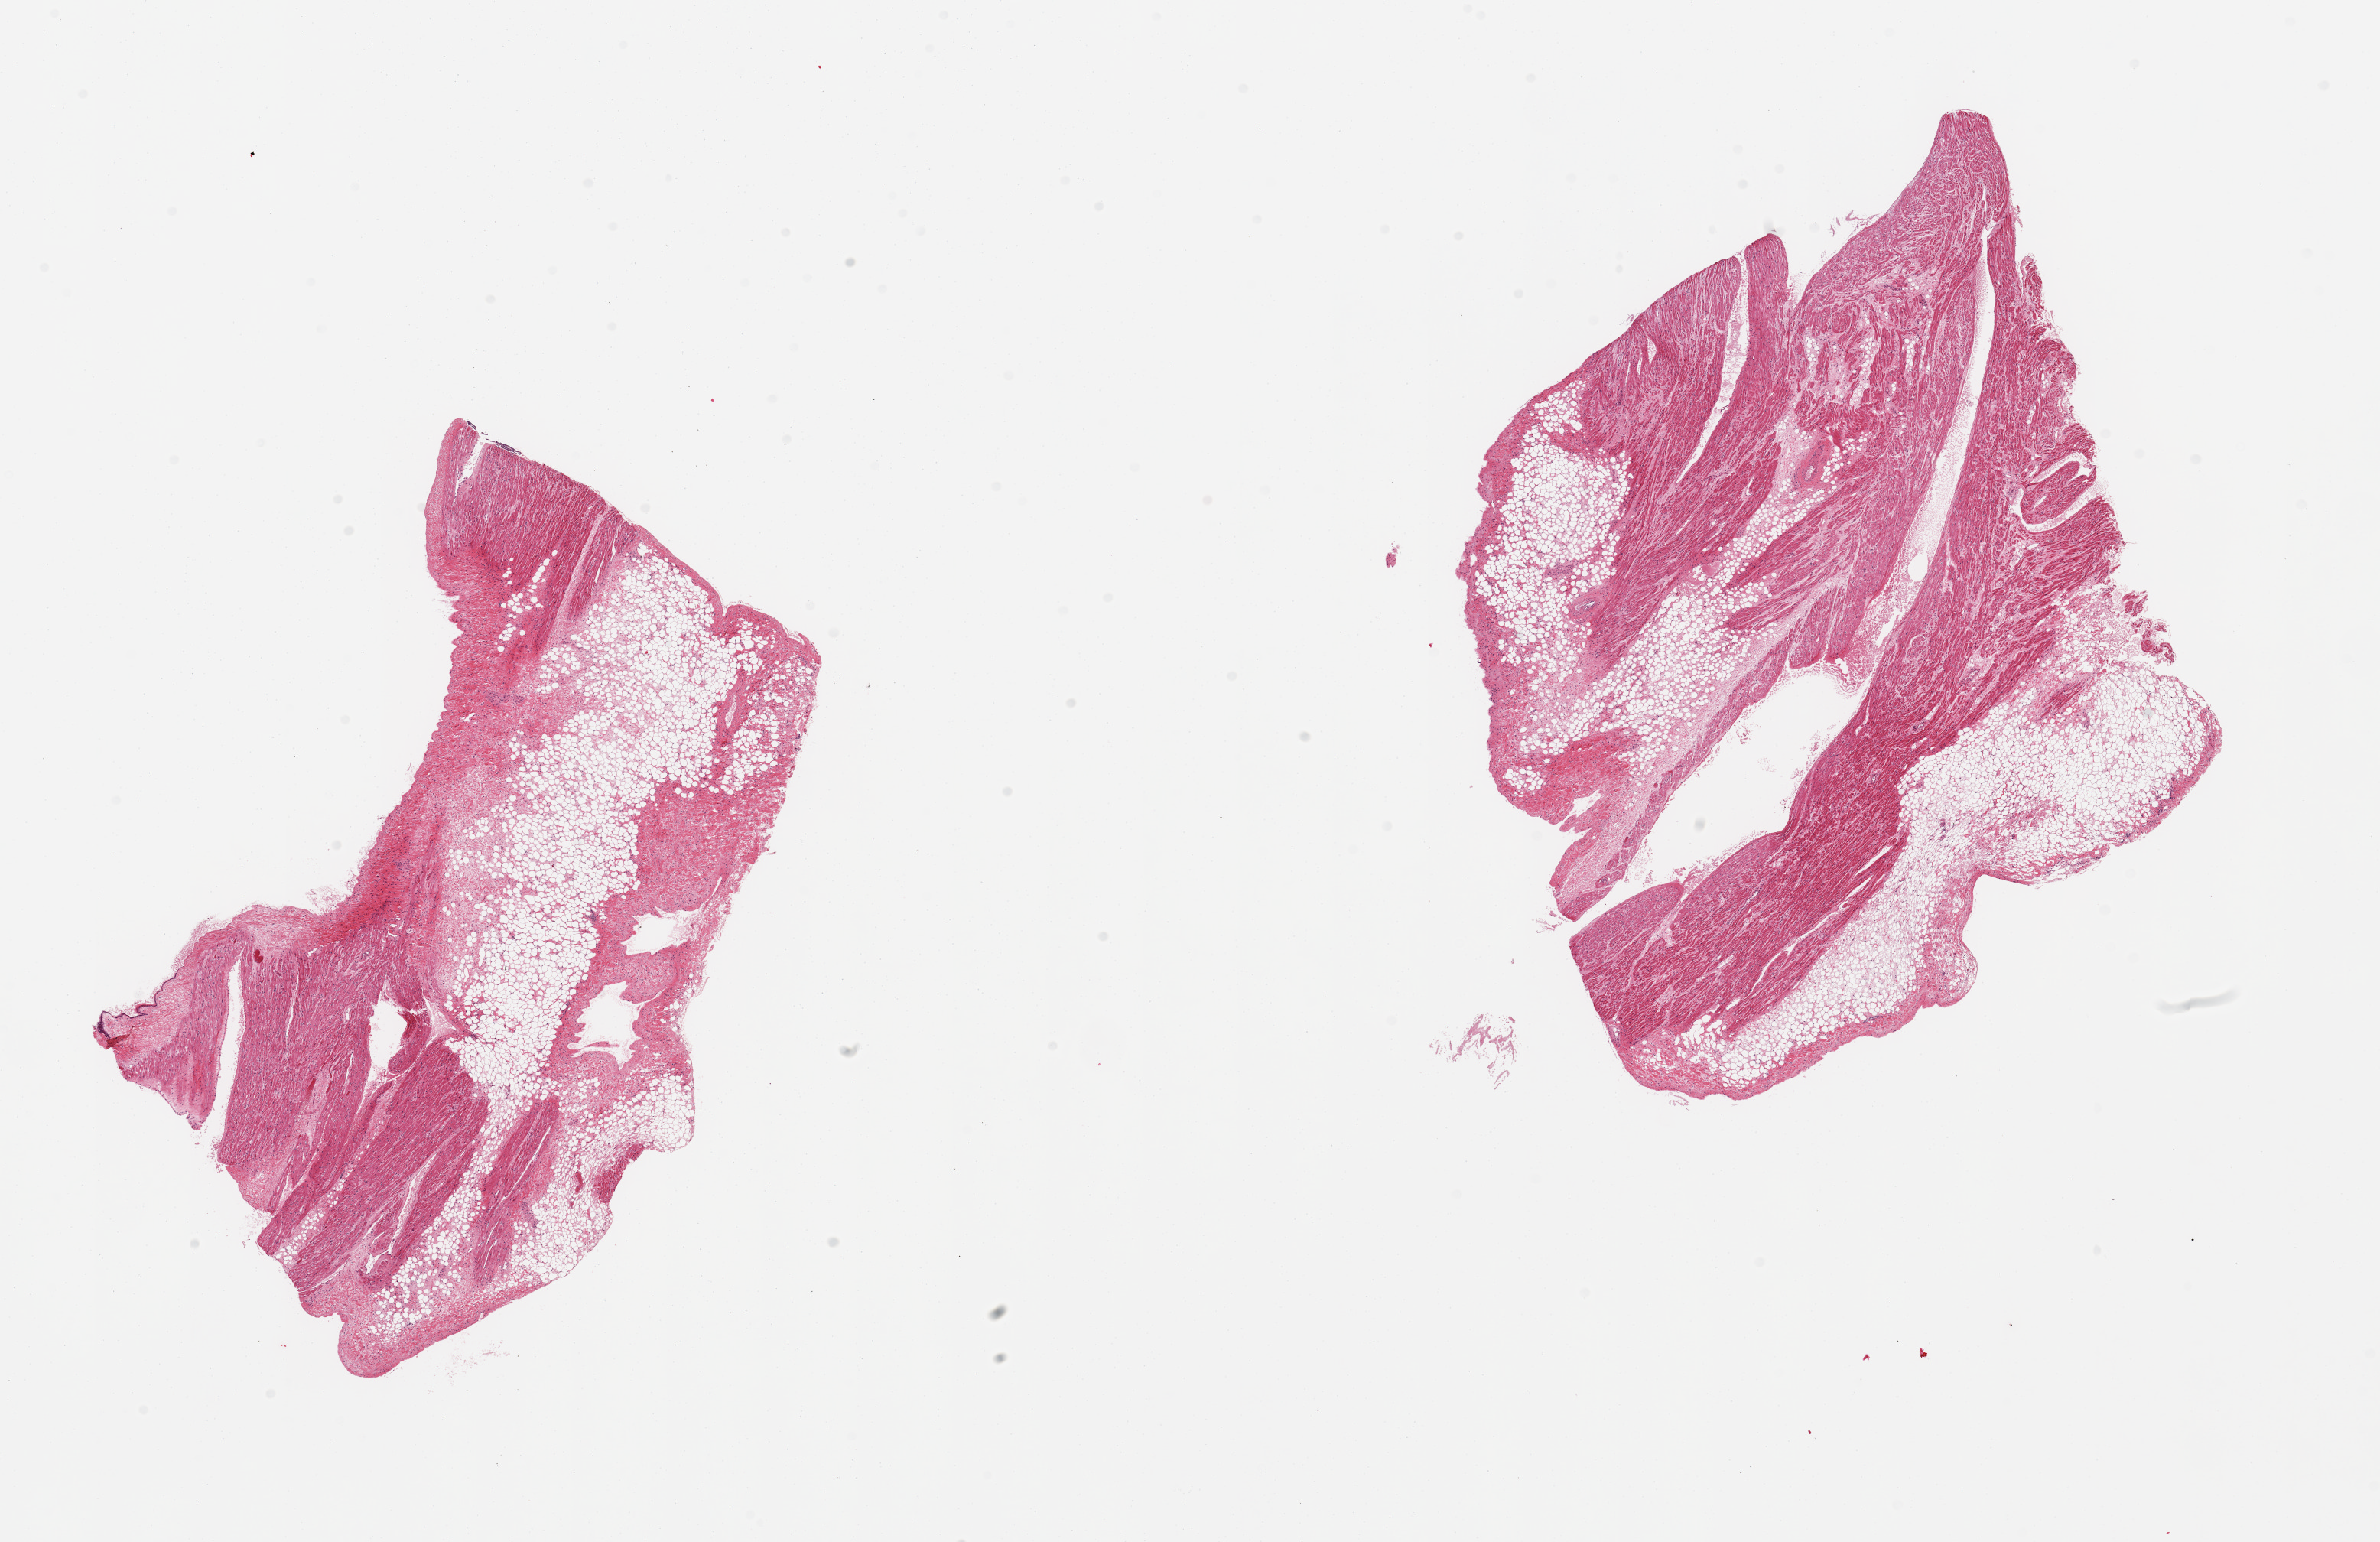
Hematoxylin and eosin (H&E) whole-slide image — a low-resolution overview of the entire scanned area, about 24.6 x 15.9 mm (acquisition: 20x scan). PAXgene-fixed, paraffin-embedded tissue. Sampled site (target tissue): auricular appendage. Tissue donor sample. Donor sex: male.
• review note (as recorded): 2 pieces; 40 and 70% fat and fibrous tissue